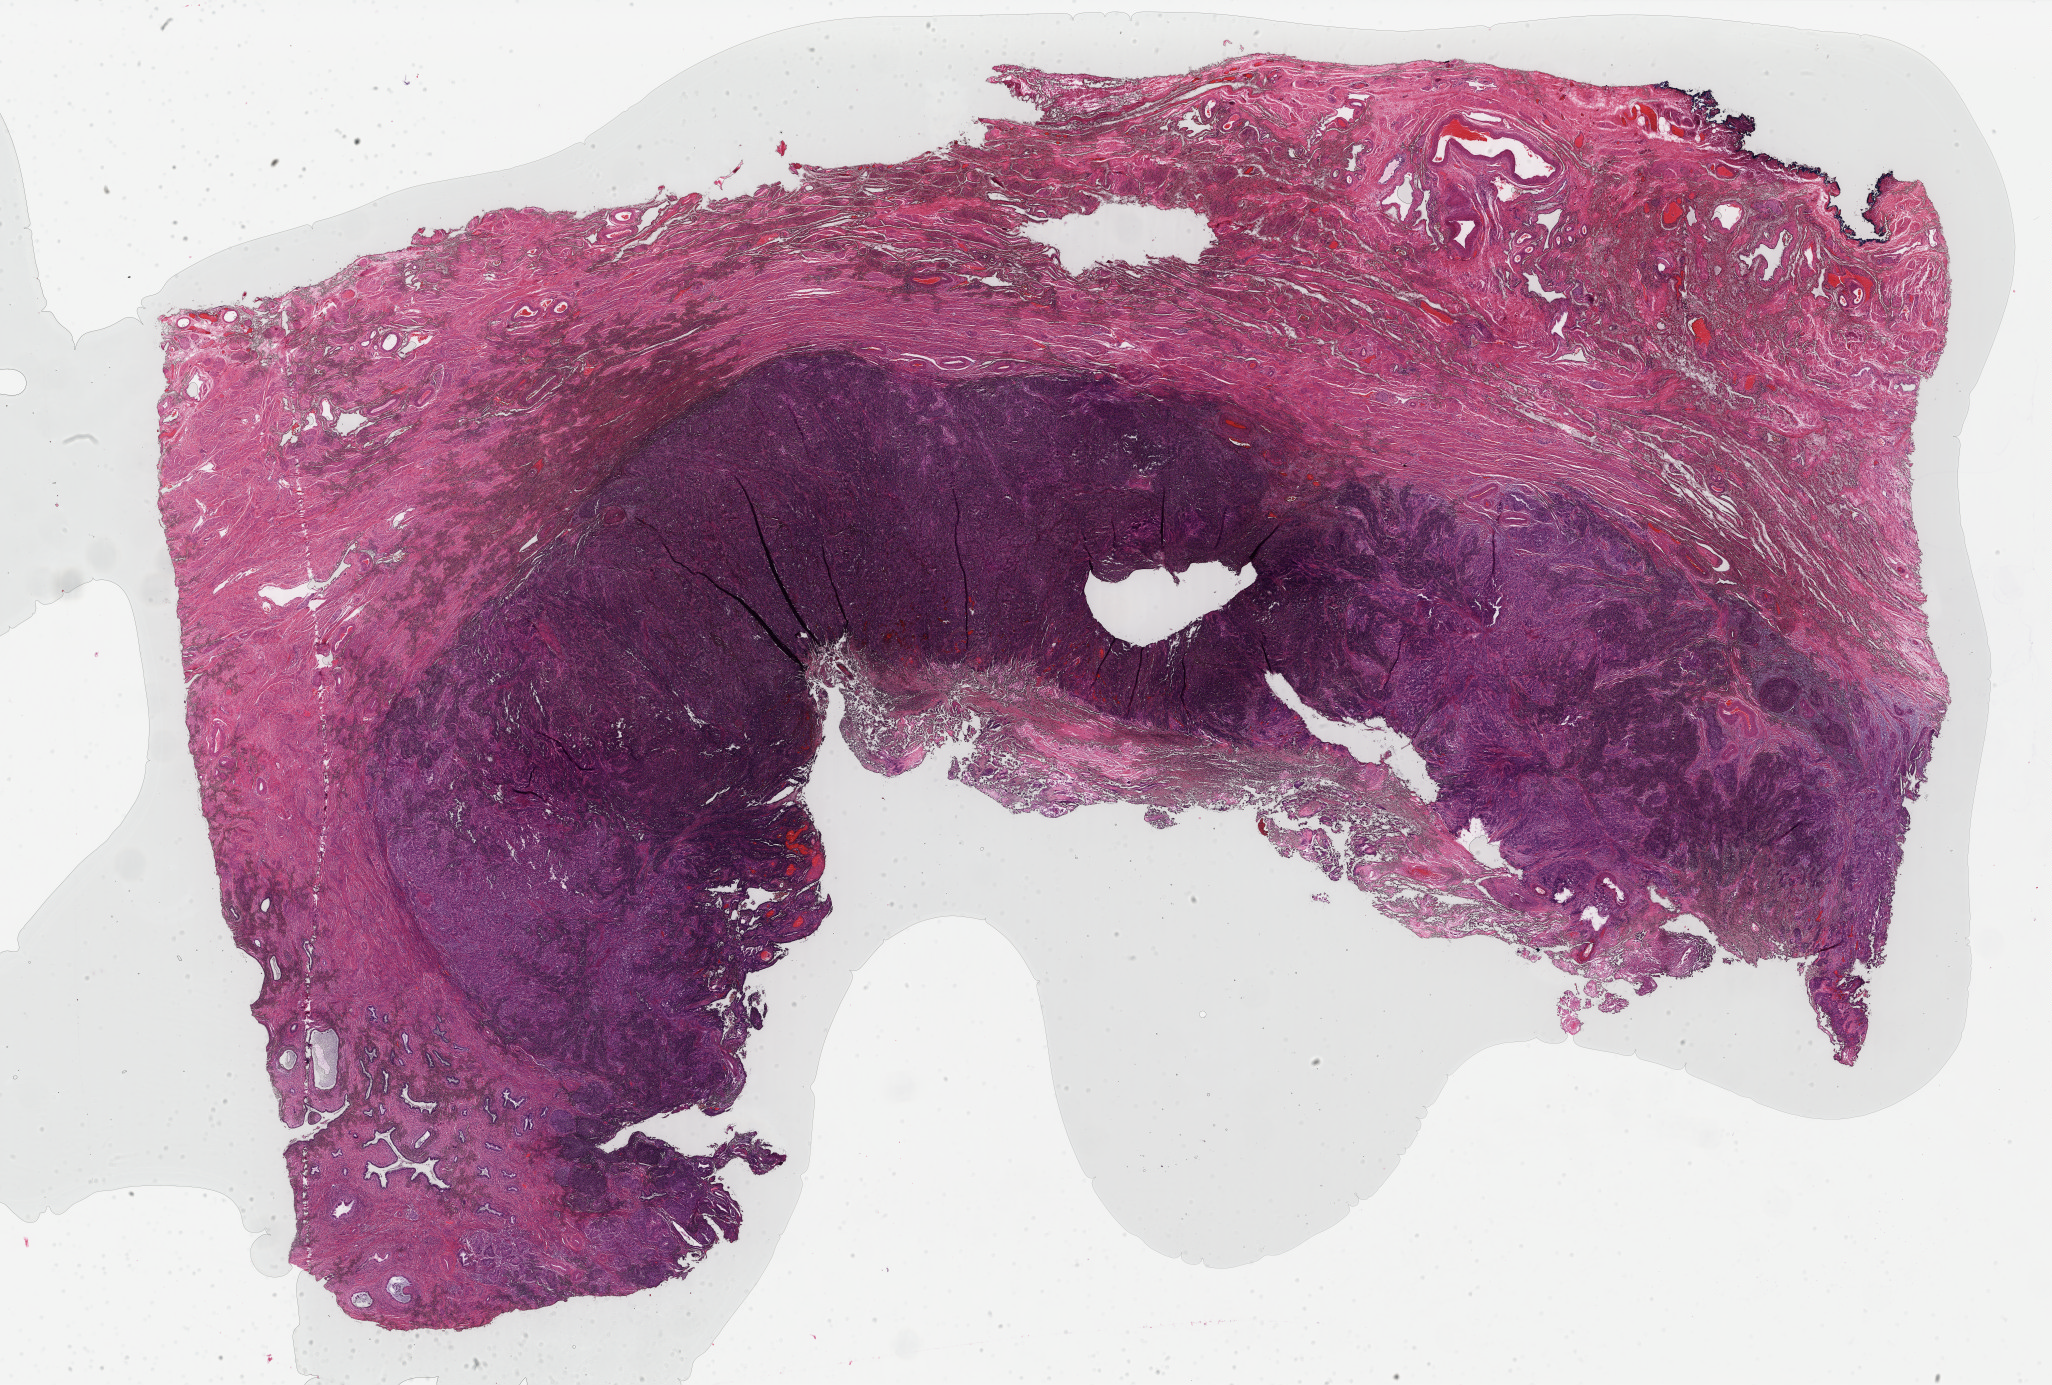
H&E whole-slide image — a low-resolution overview of the entire scanned area, about 32.6 x 22.0 mm (acquisition: 40x scan); formalin-fixed paraffin-embedded (FFPE) diagnostic section; cervix, primary tumour sample. Patient: female, age at initial diagnosis 51 years.
Histologic diagnosis: Squamous cell carcinoma, NOS.